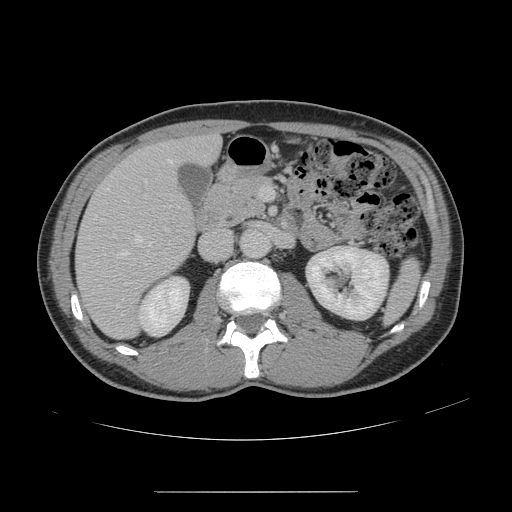
Contrast-enhanced abdominal CT, one axial slice; position 72 of 178 along the scan axis; intravenous contrast given; soft-tissue window (W 400 / L 40 HU); 2.5 mm slice thickness; 512 × 512 image matrix, field of view 401 × 401 mm. Male patient, age 53 years. Case-level facts recorded for this patient, not image findings: diagnosis: colorectal cancer liver metastases, imaged before liver resection; multiple liver metastases: yes; largest metastasis: 2.4 cm.
Structures marked on this image (outlined manually by an expert reader):
- hepatic veins: bounding box (x1, y1, x2, y2) in pixels: (96, 160, 171, 308)
- liver: (77, 137, 221, 339)
- planned liver remnant (the part of the liver to remain after resection): (189, 137, 220, 161)
- portal vein (with intrahepatic branches): (145, 187, 267, 200)